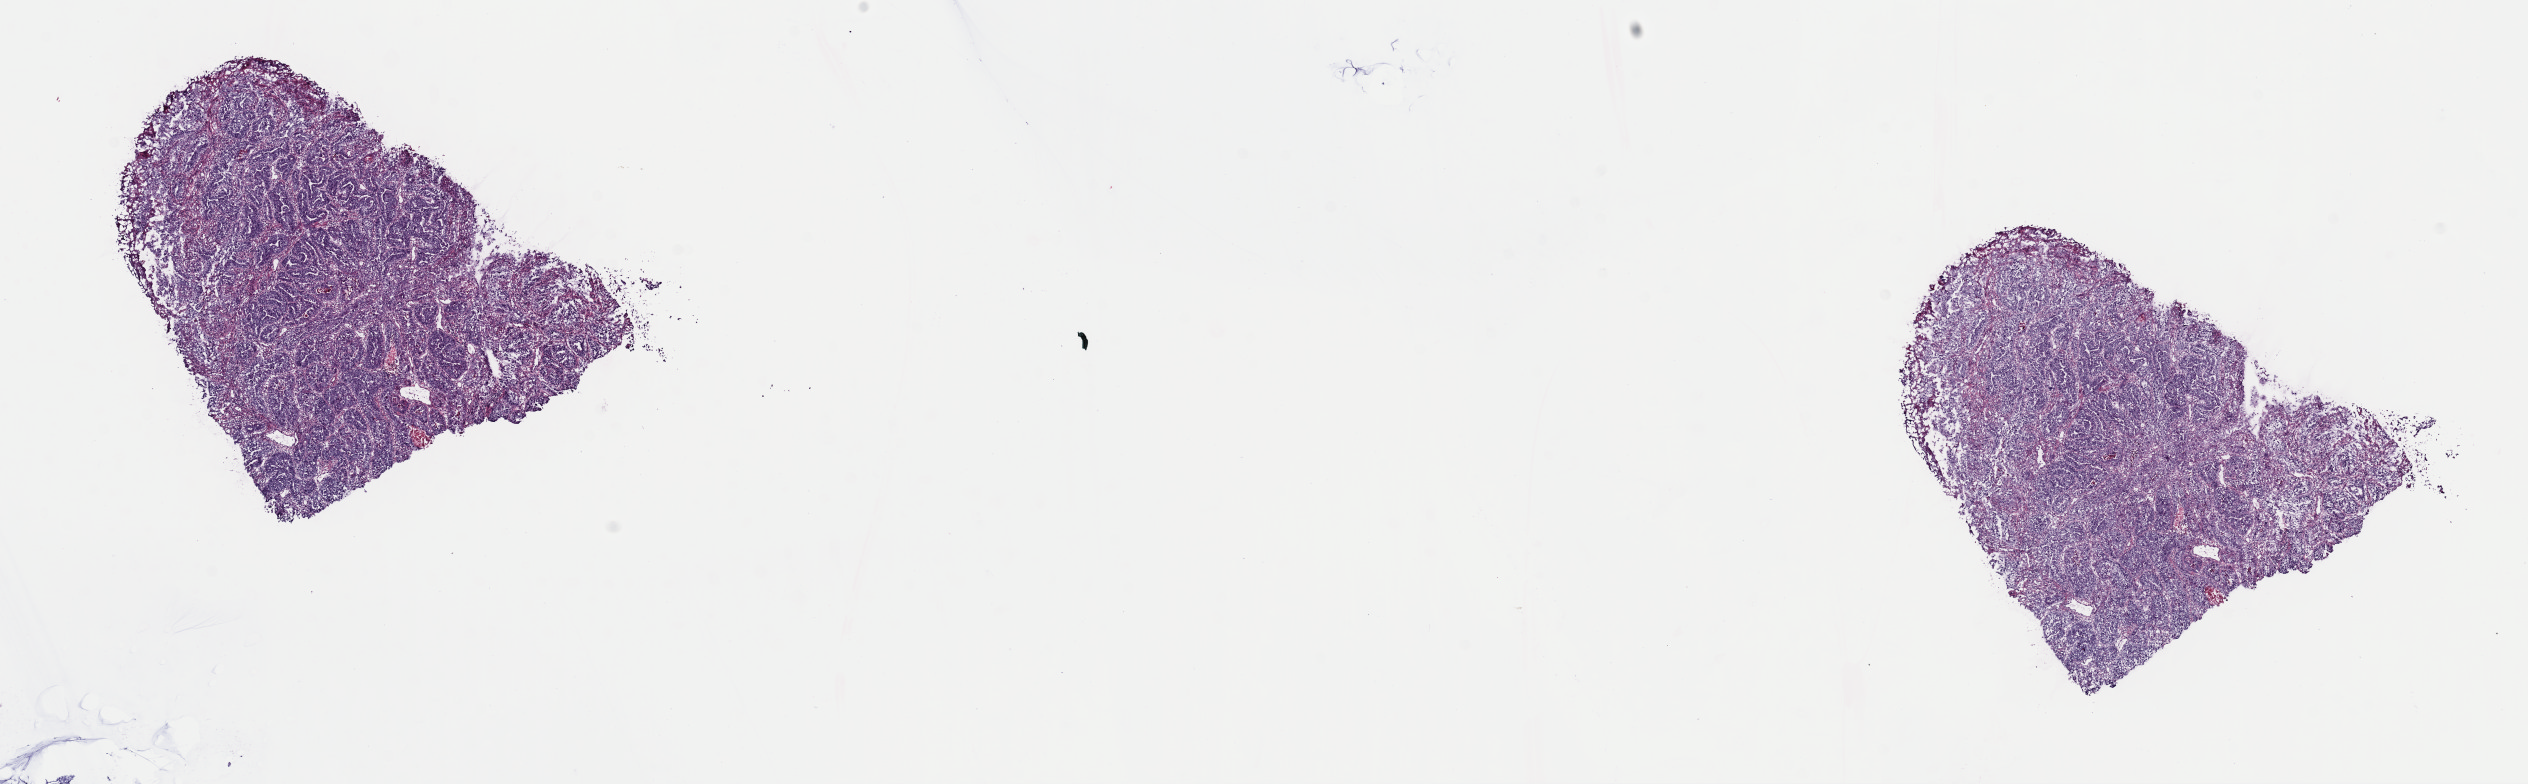
Digitized Hematoxylin and eosin (H&E) stained tissue section (whole slide) — whole scanned area (about 20.0 x 6.2 mm, acquisition: 40x scan) shown as a low-resolution overview, frozen section from the top of the tissue portion, sample: primary tumour, esophagus. Male, age 71 years at initial diagnosis. Histologic grade: GX (grade cannot be assessed). Composition of this section per pathologist review: tumour cells 75%, tumour nuclei 80%, normal cells 0%, stromal cells 20%, necrosis 5%. Infiltration values recorded for this section: lymphocyte infiltration 5%, monocyte infiltration 0%, neutrophil infiltration 0%.
Lymph nodes positive (case pathology): 0 of 9 examined. Diagnosis: Adenocarcinoma, NOS (lower third of esophagus). AJCC pathologic stage: I (7th edition).